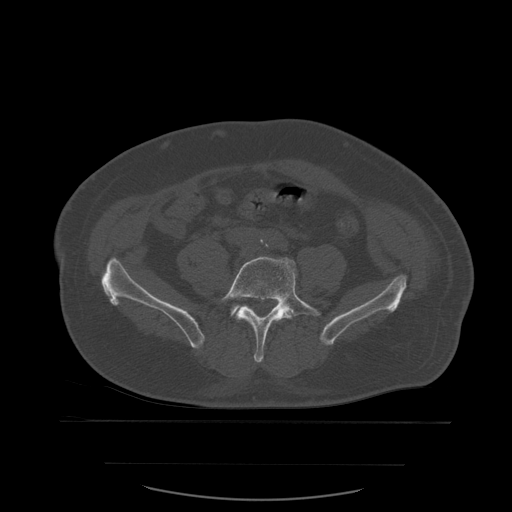
CT including the spine, one axial slice. Position 139 of 590 along the scan axis. Bone window (W 1800 / L 400 HU). 1.25 mm slice thickness. 512 × 512 image matrix, field of view 479 × 479 mm. Patient age 71 years. From the clinical record (not read from this slice): primary cancer: lung; vertebrae with lytic lesions (as recorded): T1, T2, L5, S1.
Annotated regions visible in this slice (semi-automatic segmentation, software-assisted and operator-edited):
- L5 vertebra: bounding box <219,256,321,363> (left, top, right, bottom; pixels)